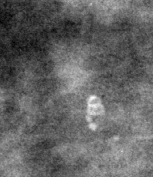
Region of interest cut from a scanned film mammogram (one marked finding); right breast; MLO view.
- Calcifications, morphology round and regular / lucent center; BI-RADS assessment category 2; subtlety rating 3 on a 1 (subtle) to 5 (obvious) scale; benign without callback (not worked up further).